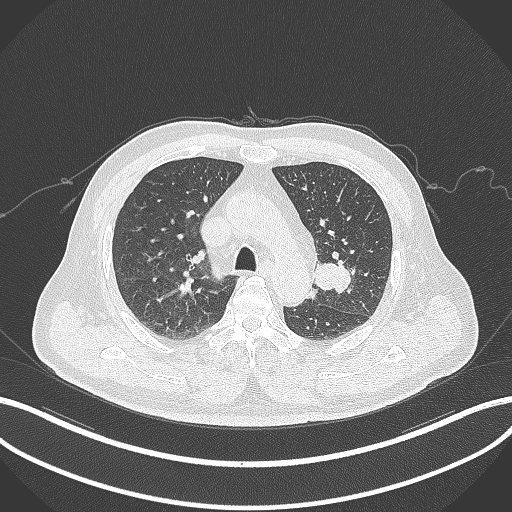
Chest CT, one axial slice; slice 211 of 286 in the series (ordered by position); 120 kVp; lung window (W 1500 / L -600 HU); 1 mm slice thickness; 512 × 512 image matrix, field of view 400 × 400 mm. Male patient, age 67 years. From the clinical record (not read from this slice): clinical TNM (as recorded): T2a N1 M0; histopathological grade: G3.
Annotated regions visible in this slice (bounding box drawn by a radiologist):
- lung tumour (recorded histology: adenocarcinoma): bounding box <310,258,357,296> (left, top, right, bottom; pixels)